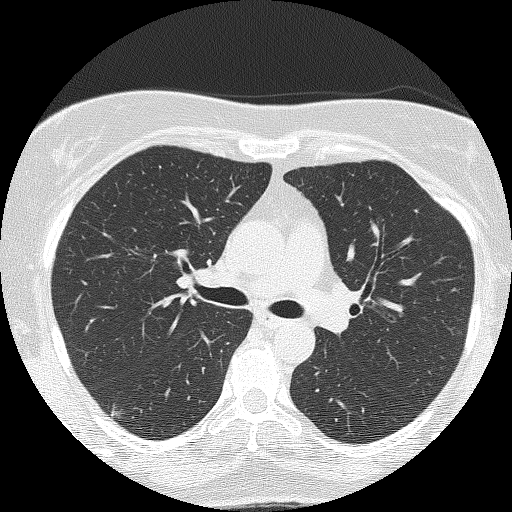
Chest CT (low-dose screening protocol), one axial image, second annual screen, lung window (W 1500 / L -600 HU), lung (sharp) reconstruction kernel (FC51), slice 56 of 143 in the series. Female participant, aged 58 years at enrolment. Former smoker at enrolment.
- Lesion marked by an expert reader, bounding box [x1, y1, x2, y2] px = [94, 393, 141, 428].
- The screening reader recorded 2 non-calcified nodules or masses ≥4 mm on this exam (right upper lobe, right upper lobe); which of them this box marks is not recorded.
- Participant outcome: lung cancer diagnosed 264 days after this screen — adenocarcinoma, NOS, right lower lobe, well differentiated (G1), stage IB (AJCC 6th edition), 10 mm at pathology.